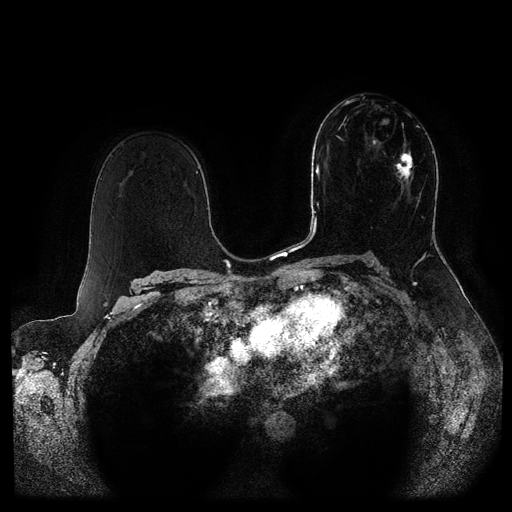
Breast MRI (dynamic contrast-enhanced, multi-phase), one axial slice; slice 58 of 116 in the series (ordered by position); dynamic contrast-enhanced series, time point 2 of 5 at this slice position (early post-contrast); 1.5 T; TE 2.6 ms, TR 5.3 ms; 512 × 512 image matrix, field of view 370 × 370 mm. Patient: female, 51 years.
Outlined on this slice (semi-automatically segmented with operator editing):
- breast lesion (labelled 'tumour' in the annotation; benign lesions carry a separate 'benign' label): bounding box (x1, y1, x2, y2) in pixels: (373, 122, 414, 183)